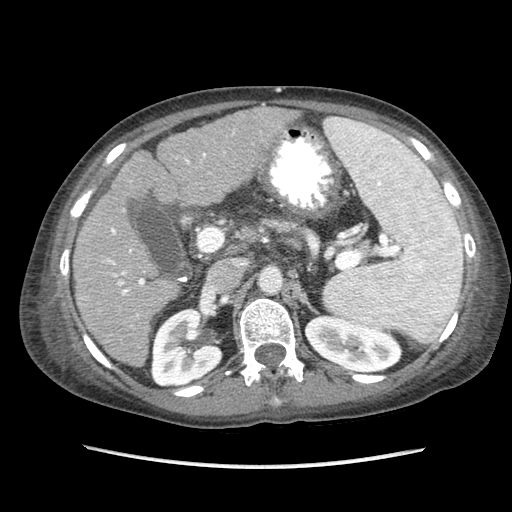
Contrast-enhanced abdominal CT (liver protocol), one axial slice. Position 43 of 87 along the scan axis. 120 kVp. Soft-tissue window (W 400 / L 40 HU). 2.5 mm slice thickness. 512 × 512 image matrix. Case-level facts recorded for this patient, not image findings: diagnosis: hepatocellular carcinoma (patient treated with transarterial chemoembolisation; whether this scan precedes or follows treatment is not stated here); TNM stage (as recorded): Stage-IIIB.
Outlined on this slice (semi-automatically segmented with operator editing):
- liver parenchyma outside the tumour (the mass and vessels are separate outlines, so this box may not span the whole liver): bounding box <72,106,298,366> (left, top, right, bottom; pixels)
- liver vessels: <107,133,234,296>